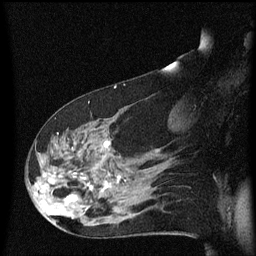
Breast MRI (dynamic contrast-enhanced), one sagittal slice; position 36 of 60 along the scan axis; dynamic contrast-enhanced series, image 2 of 3 at this slice position (ordered by acquisition); 1.5 T; TE 4.2 ms, TR 8.4 ms; 2 mm slice thickness; 256 × 256 image matrix, field of view 200 × 200 mm. Female patient, age 48 years.
Outlined on this slice (semi-automatic segmentation, software-assisted and operator-edited):
- analysis volume of interest (the breast-tissue region the enhancement analysis was run in; not a lesion): bounding box (x1, y1, x2, y2) in pixels: (31, 116, 134, 225)
- tumour enhancement mask (voxels above the 70 % enhancement threshold inside the analysis volume of interest): (66, 142, 120, 203)